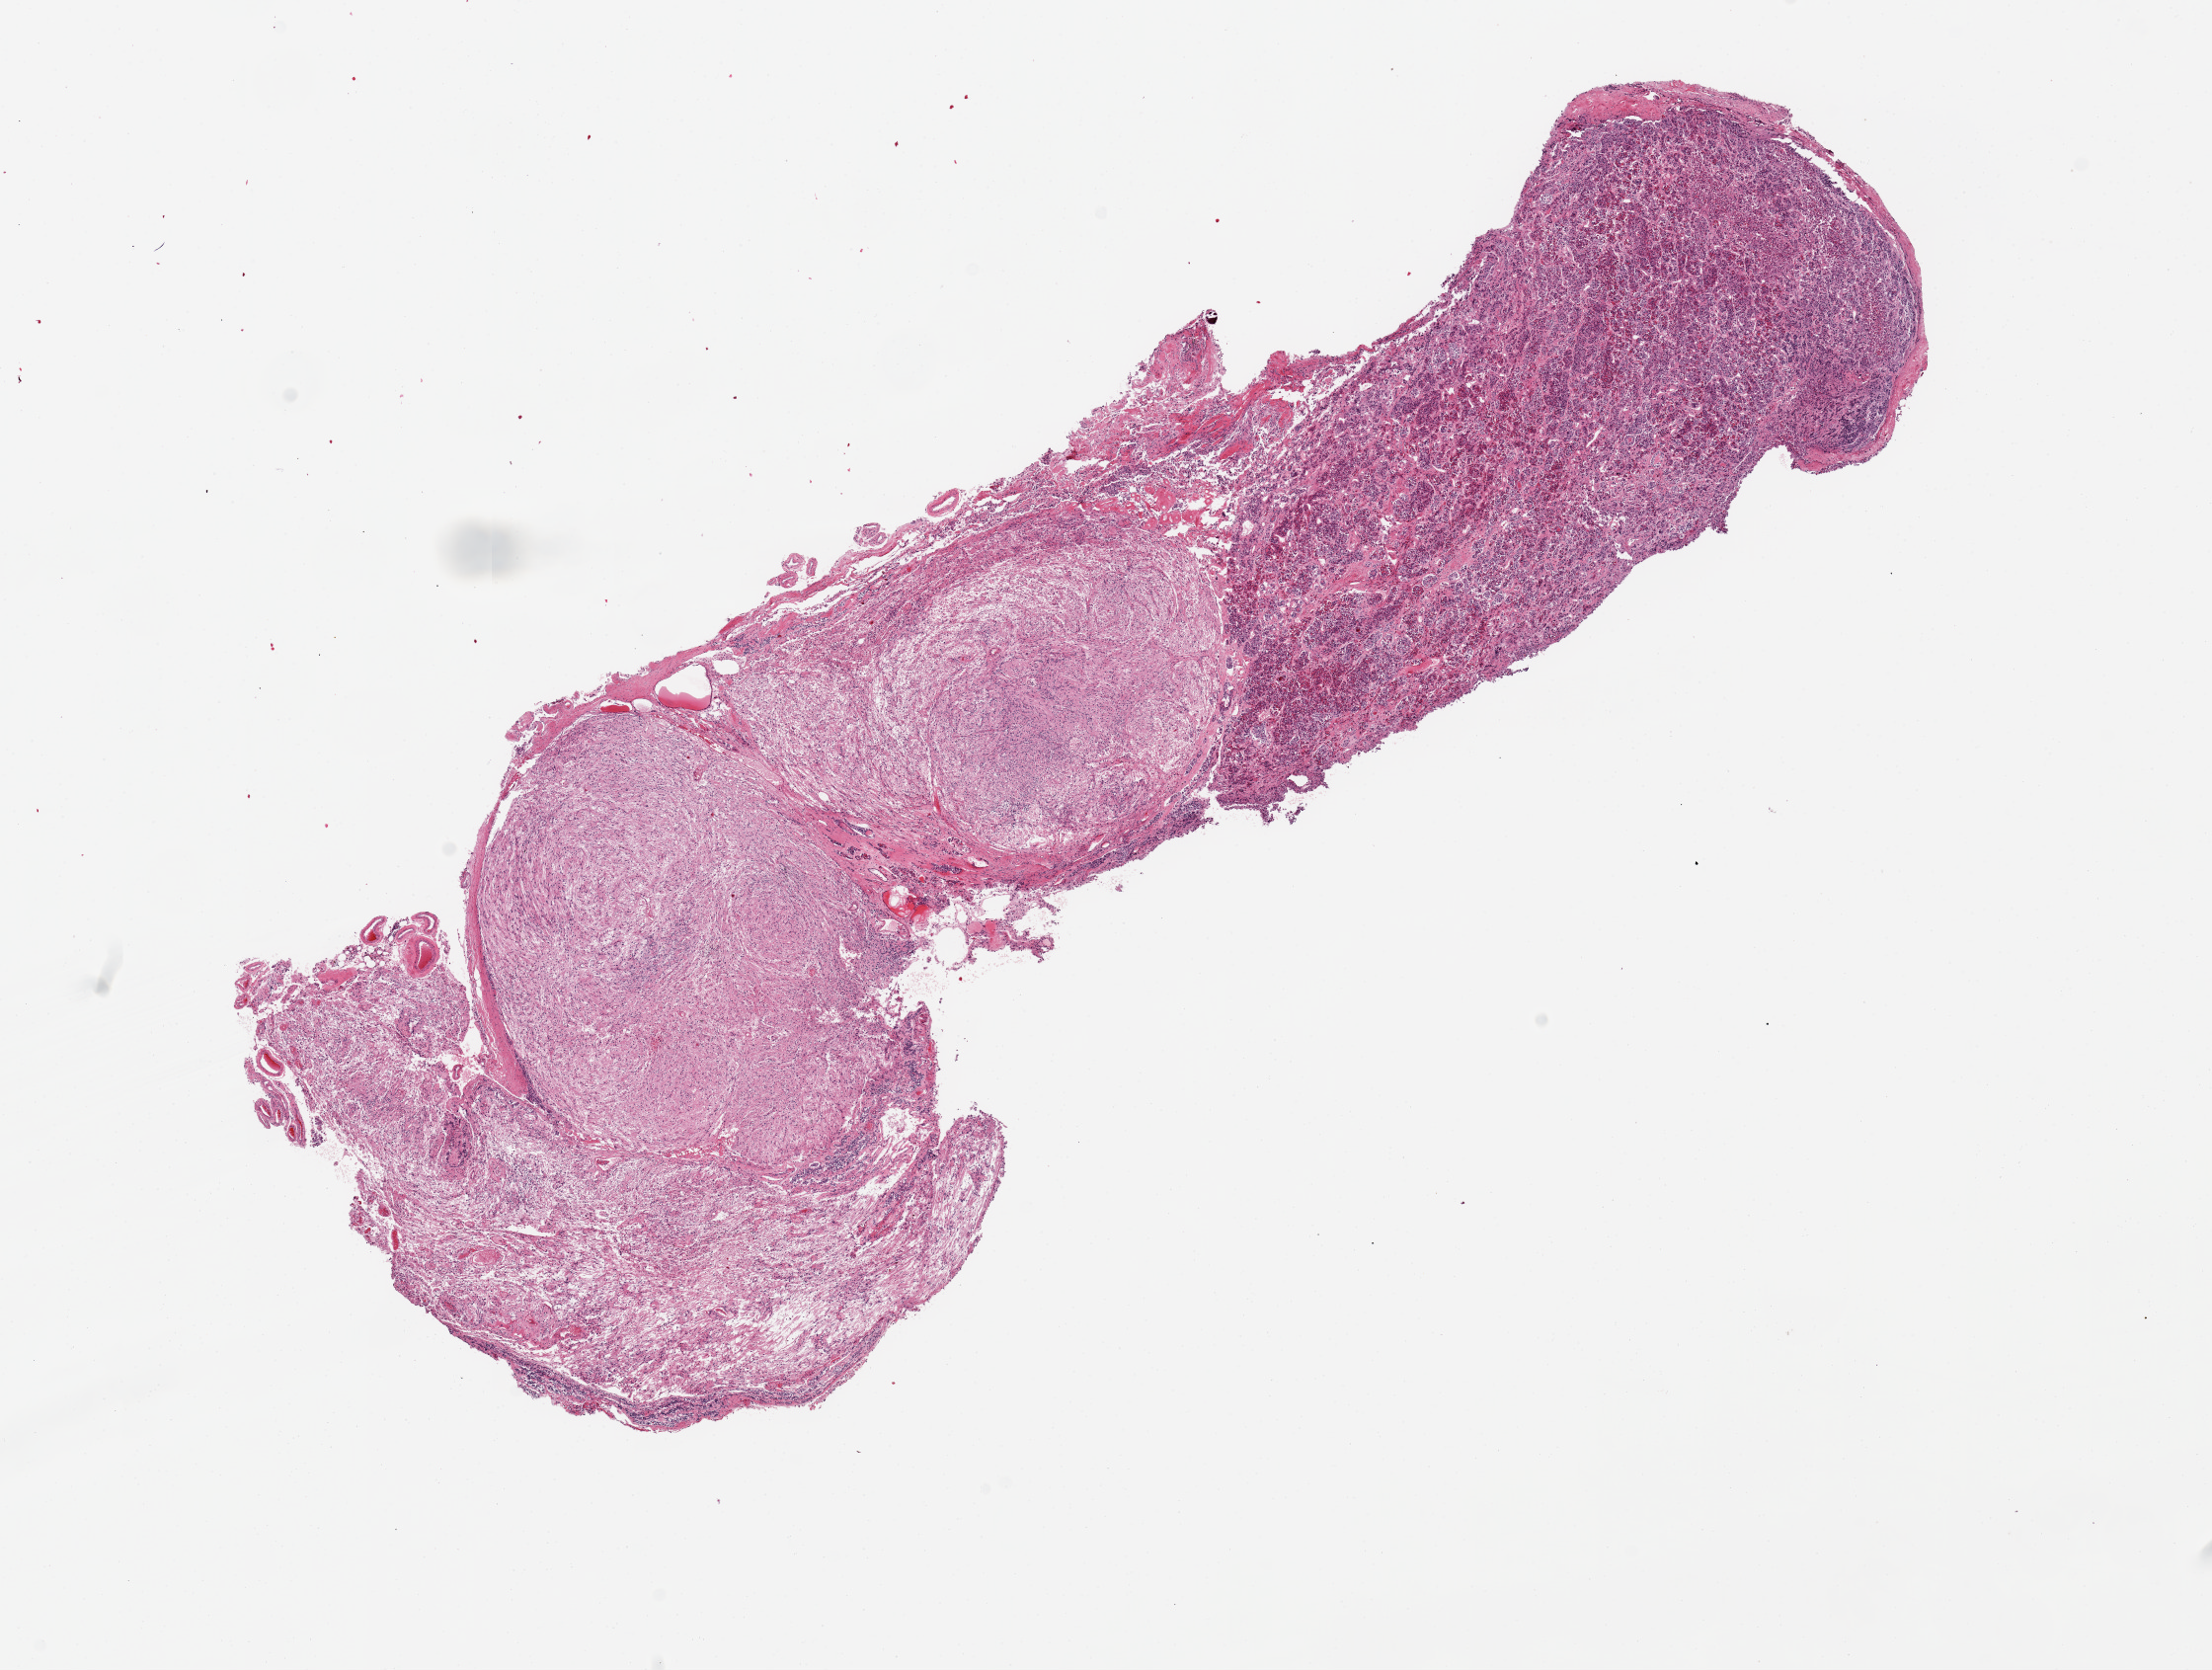
Digitized H&E-stained section, brightfield, a low-resolution overview of the entire scanned area, about 17.7 x 13.4 mm (from a 20x scan); PAXgene-fixed paraffin-embedded (PFPE) section; target tissue: pituitary; donor tissue sample.
Review note (as recorded): 1 piece 15x6mm; 50% neurohypophysis.